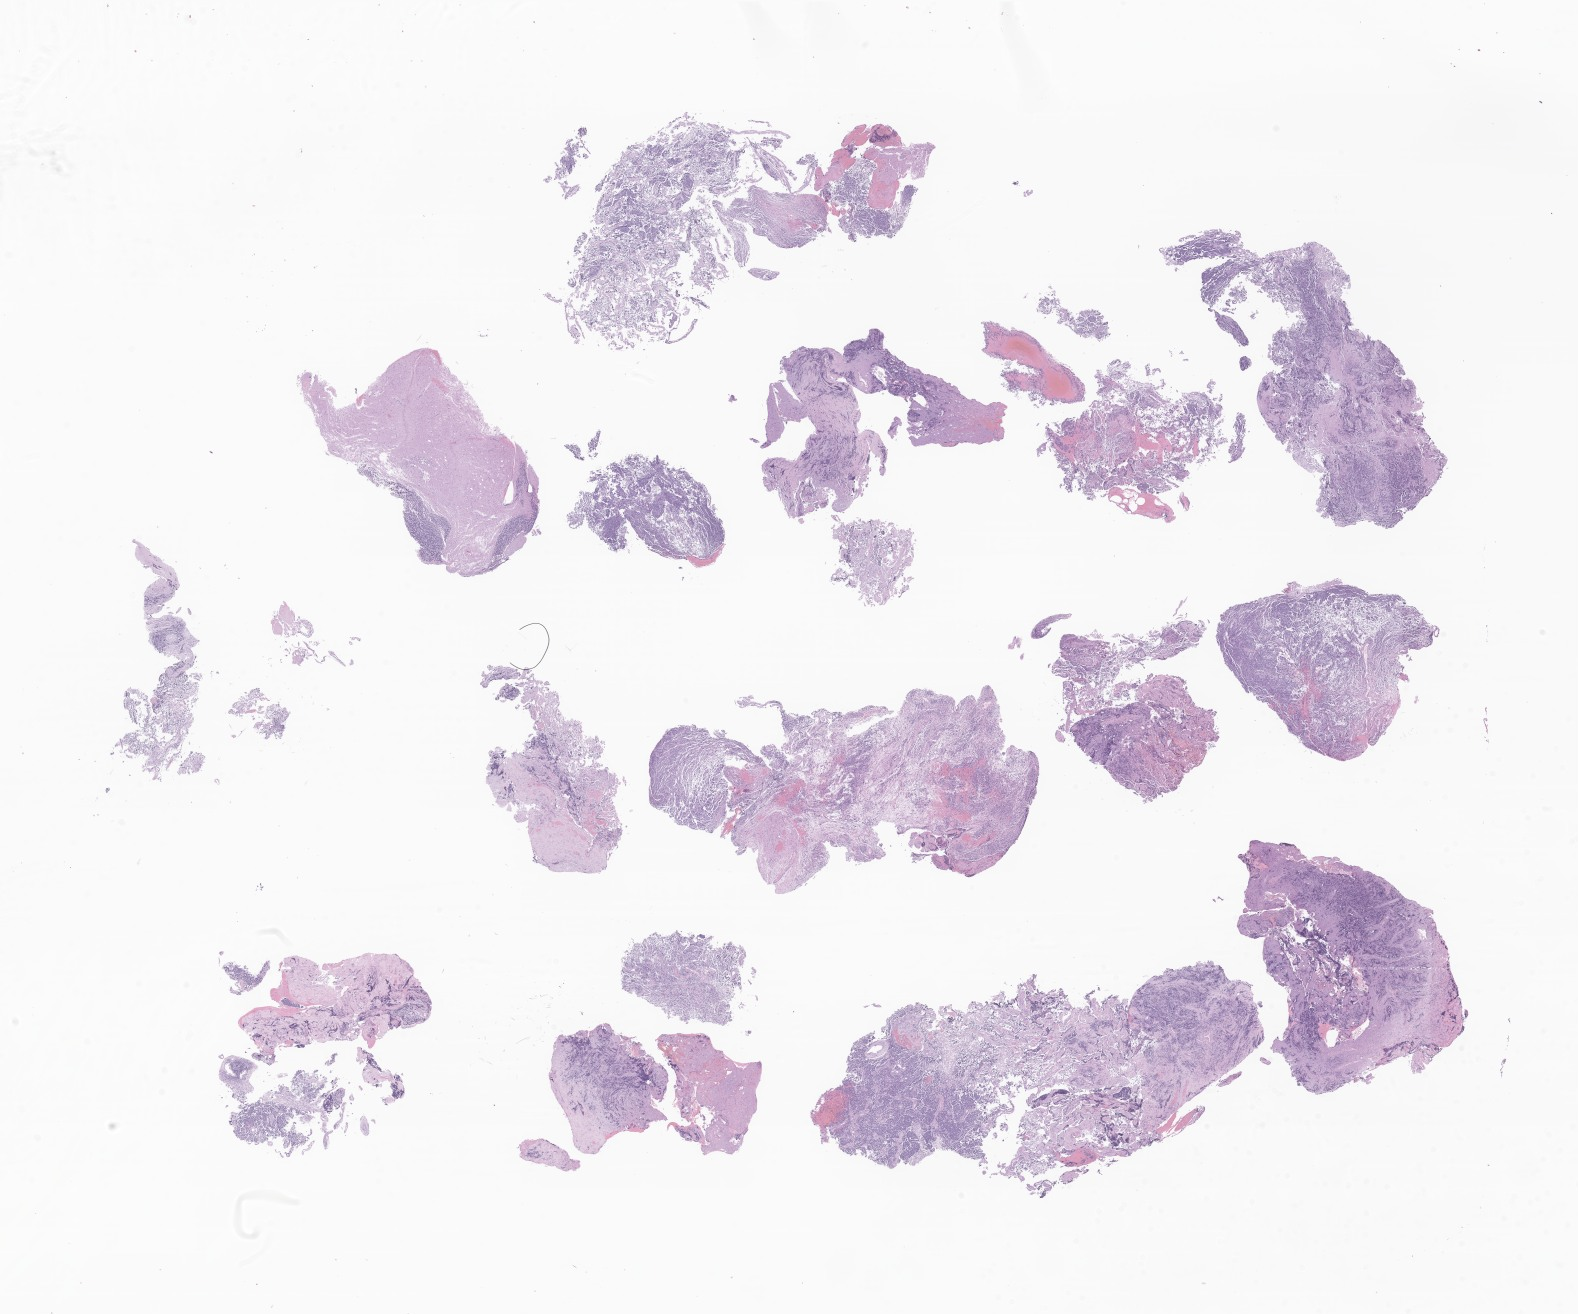
H&E whole-slide image of tumor tissue from the brain — low-resolution overview of the scanned area, about 26.6 x 22.2 mm, formalin-fixed paraffin-embedded section. Patient: male, age 87 months (7 years 3 months).
Diagnosis: Medulloblastoma, NOS.